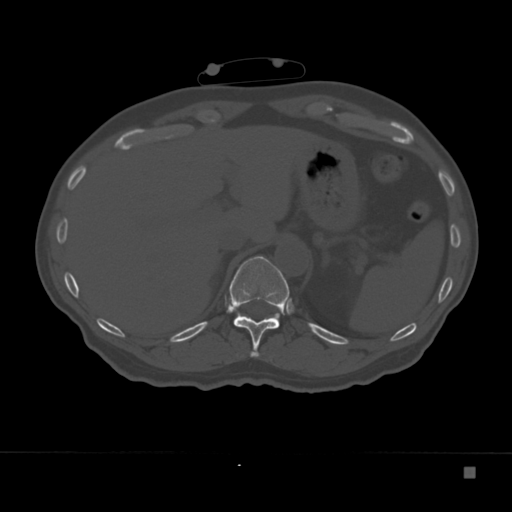
CT including the spine, one axial slice; position 150 of 332 along the scan axis; bone window (W 1800 / L 400 HU); 1.5 mm slice thickness; 512 × 512 image matrix, field of view 389 × 389 mm. Patient: male, 72 years. From the clinical record (not read from this slice): primary cancer: skeletal.
Annotated regions visible in this slice (semi-automatic segmentation, software-assisted and operator-edited):
- T11 vertebra: bounding box [x1, y1, x2, y2] px = [229, 256, 289, 357]
- T12 vertebra: [278, 316, 280, 327]